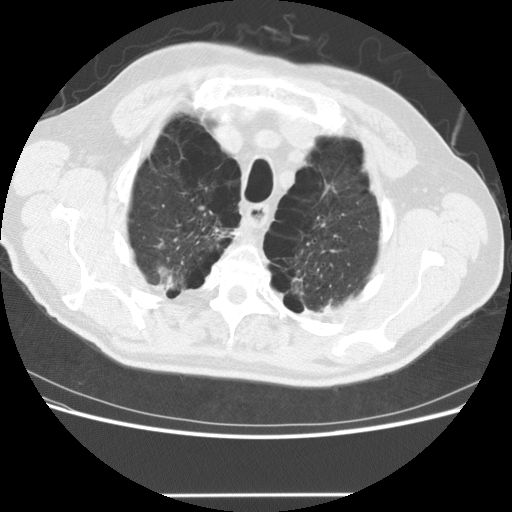
Low-dose screening chest CT, axial slice; third annual screen; lung window (W 1500 / L -600 HU); 2.5 mm slice thickness; 120 kVp; slice 32 of 151 in the series; 512 × 512 image matrix, field of view 360 × 360 mm. Male participant, aged 68 years at enrolment. Former smoker at enrolment.
• Expert reader's lesion annotation, bounding box <127,218,213,301> (left, top, right, bottom; pixels).
• The screening reader recorded 2 non-calcified nodules or masses ≥4 mm on this exam; which of them this box marks is not recorded.
• Later outcome: lung cancer diagnosed 301 days after this screen — large cell carcinoma, NOS, right upper lobe, poorly differentiated (G3), stage IV (AJCC 6th edition).